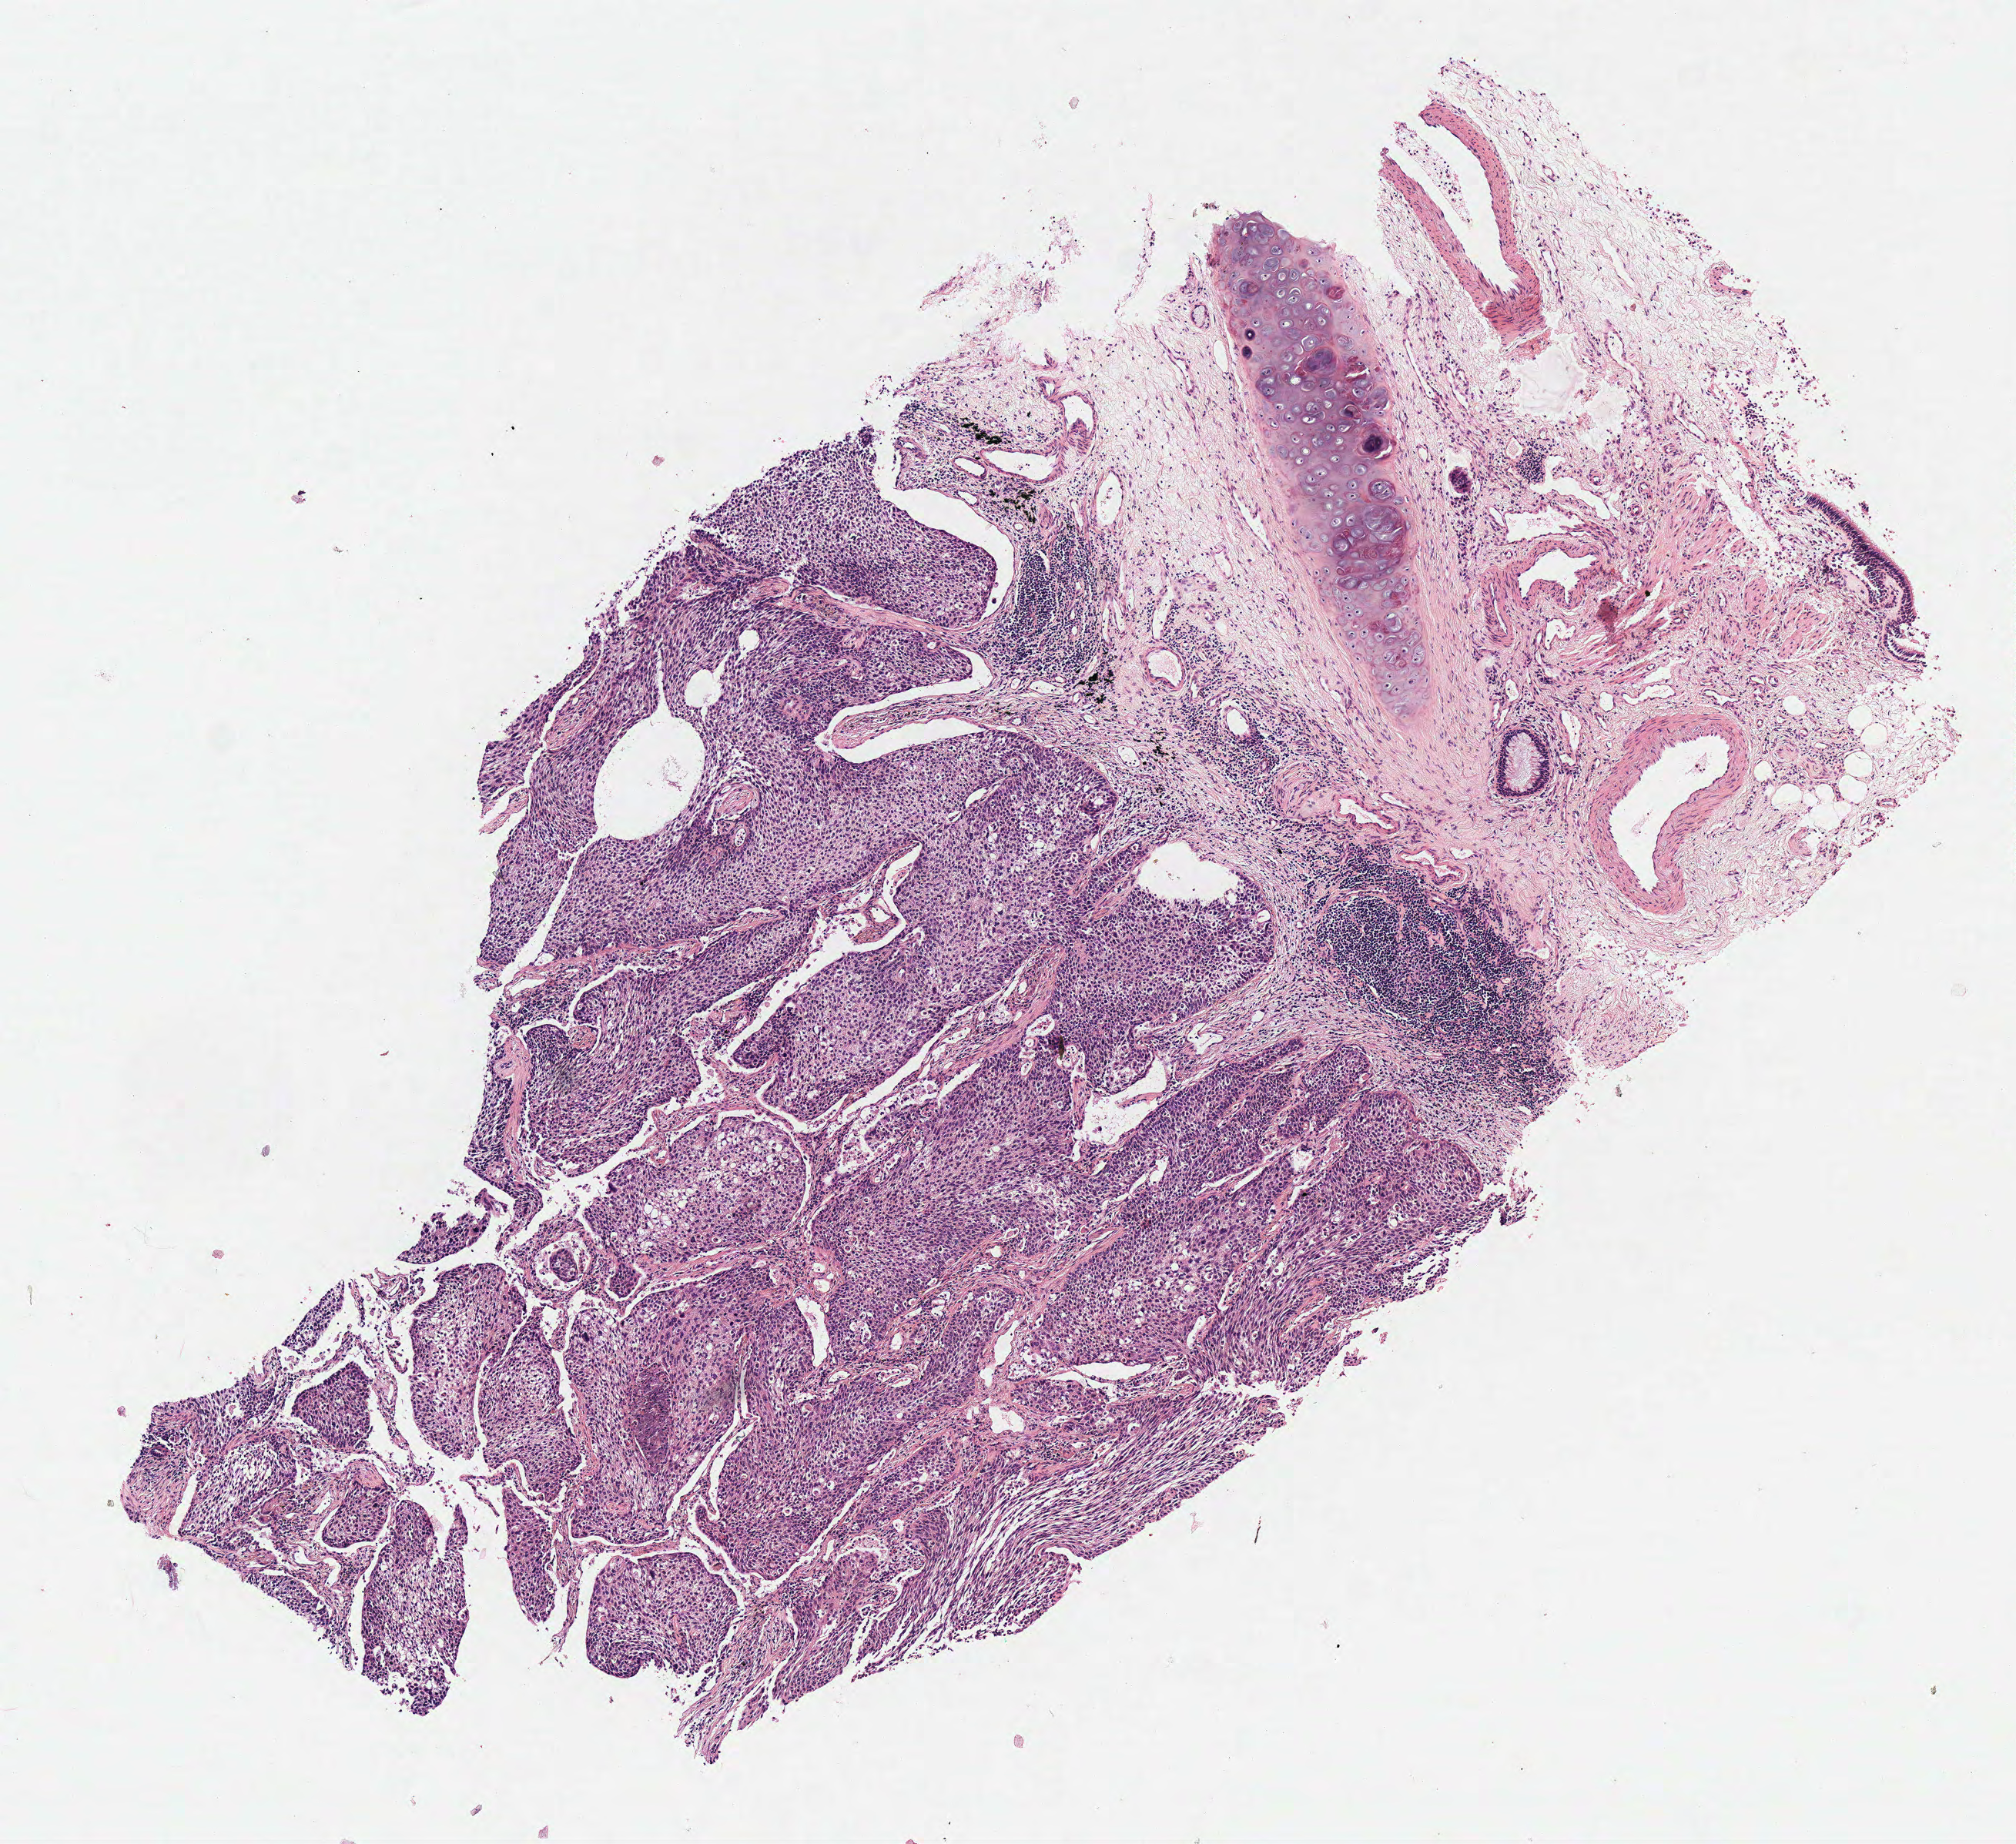
Digitized H&E tissue section (whole slide) — a low-resolution overview of the entire scanned area, about 5.2 x 4.7 mm (slide scanned at 40x), frozen section from the top of the tissue portion, lung, primary tumour sample. Patient: male, age at initial diagnosis 74 years.
Diagnosis: Squamous cell carcinoma, NOS (lower lobe, lung).